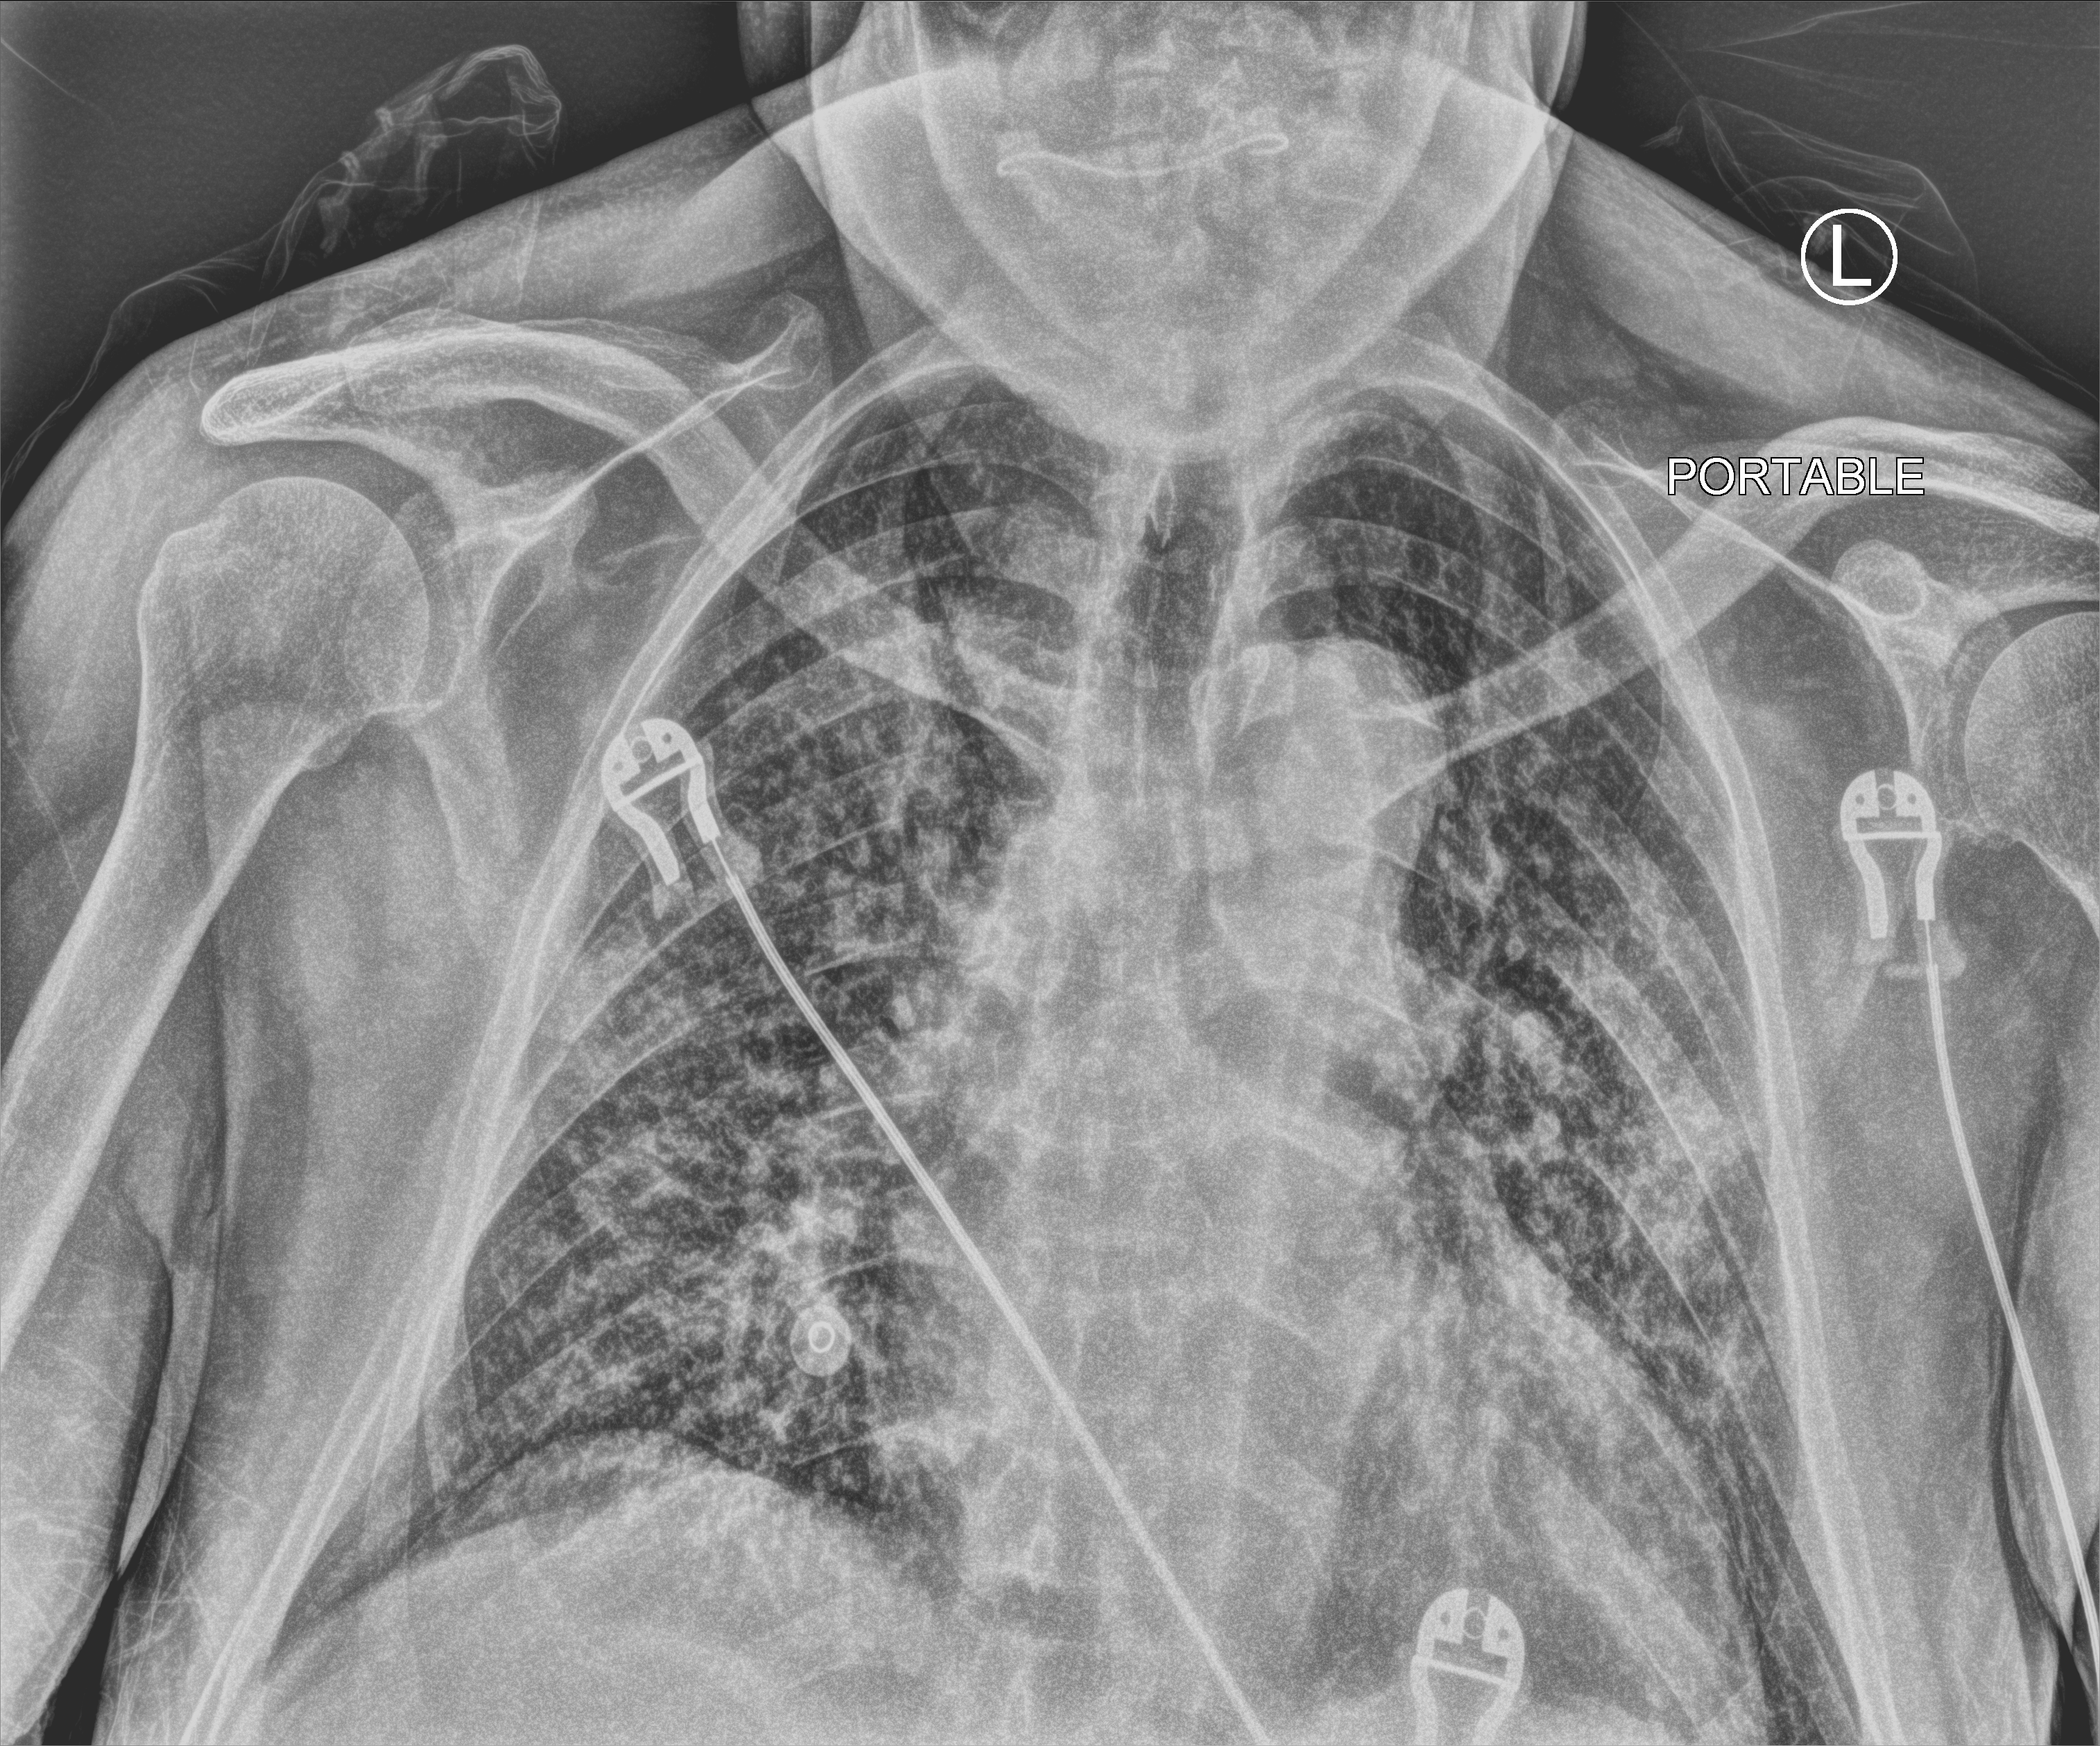
Bedside chest radiograph (computed radiography); anteroposterior (AP) projection. Male patient hospitalised with COVID-19, age 60–74 years.
Hospital-stay facts (about this admission, not read from this image; timing relative to this image not recorded):
- hypertension (admission record): yes
- diabetes (admission record): yes